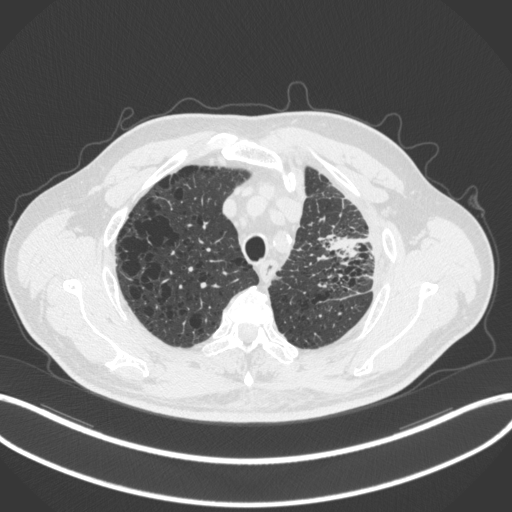
Chest CT, one axial slice. Position 249 of 286 along the scan axis. Reconstruction kernel B31f. 120 kVp. Lung window (W 1500 / L -600 HU). 512 × 512 image matrix, field of view 400 × 400 mm. Male patient, age 68 years. Case-level facts recorded for this patient, not image findings: clinical TNM (as recorded): T3 N3 M1.
Structures marked on this image (bounding box drawn by a radiologist):
- lung tumour (recorded histology: adenocarcinoma): bounding box [x1, y1, x2, y2] px = [322, 229, 361, 264]